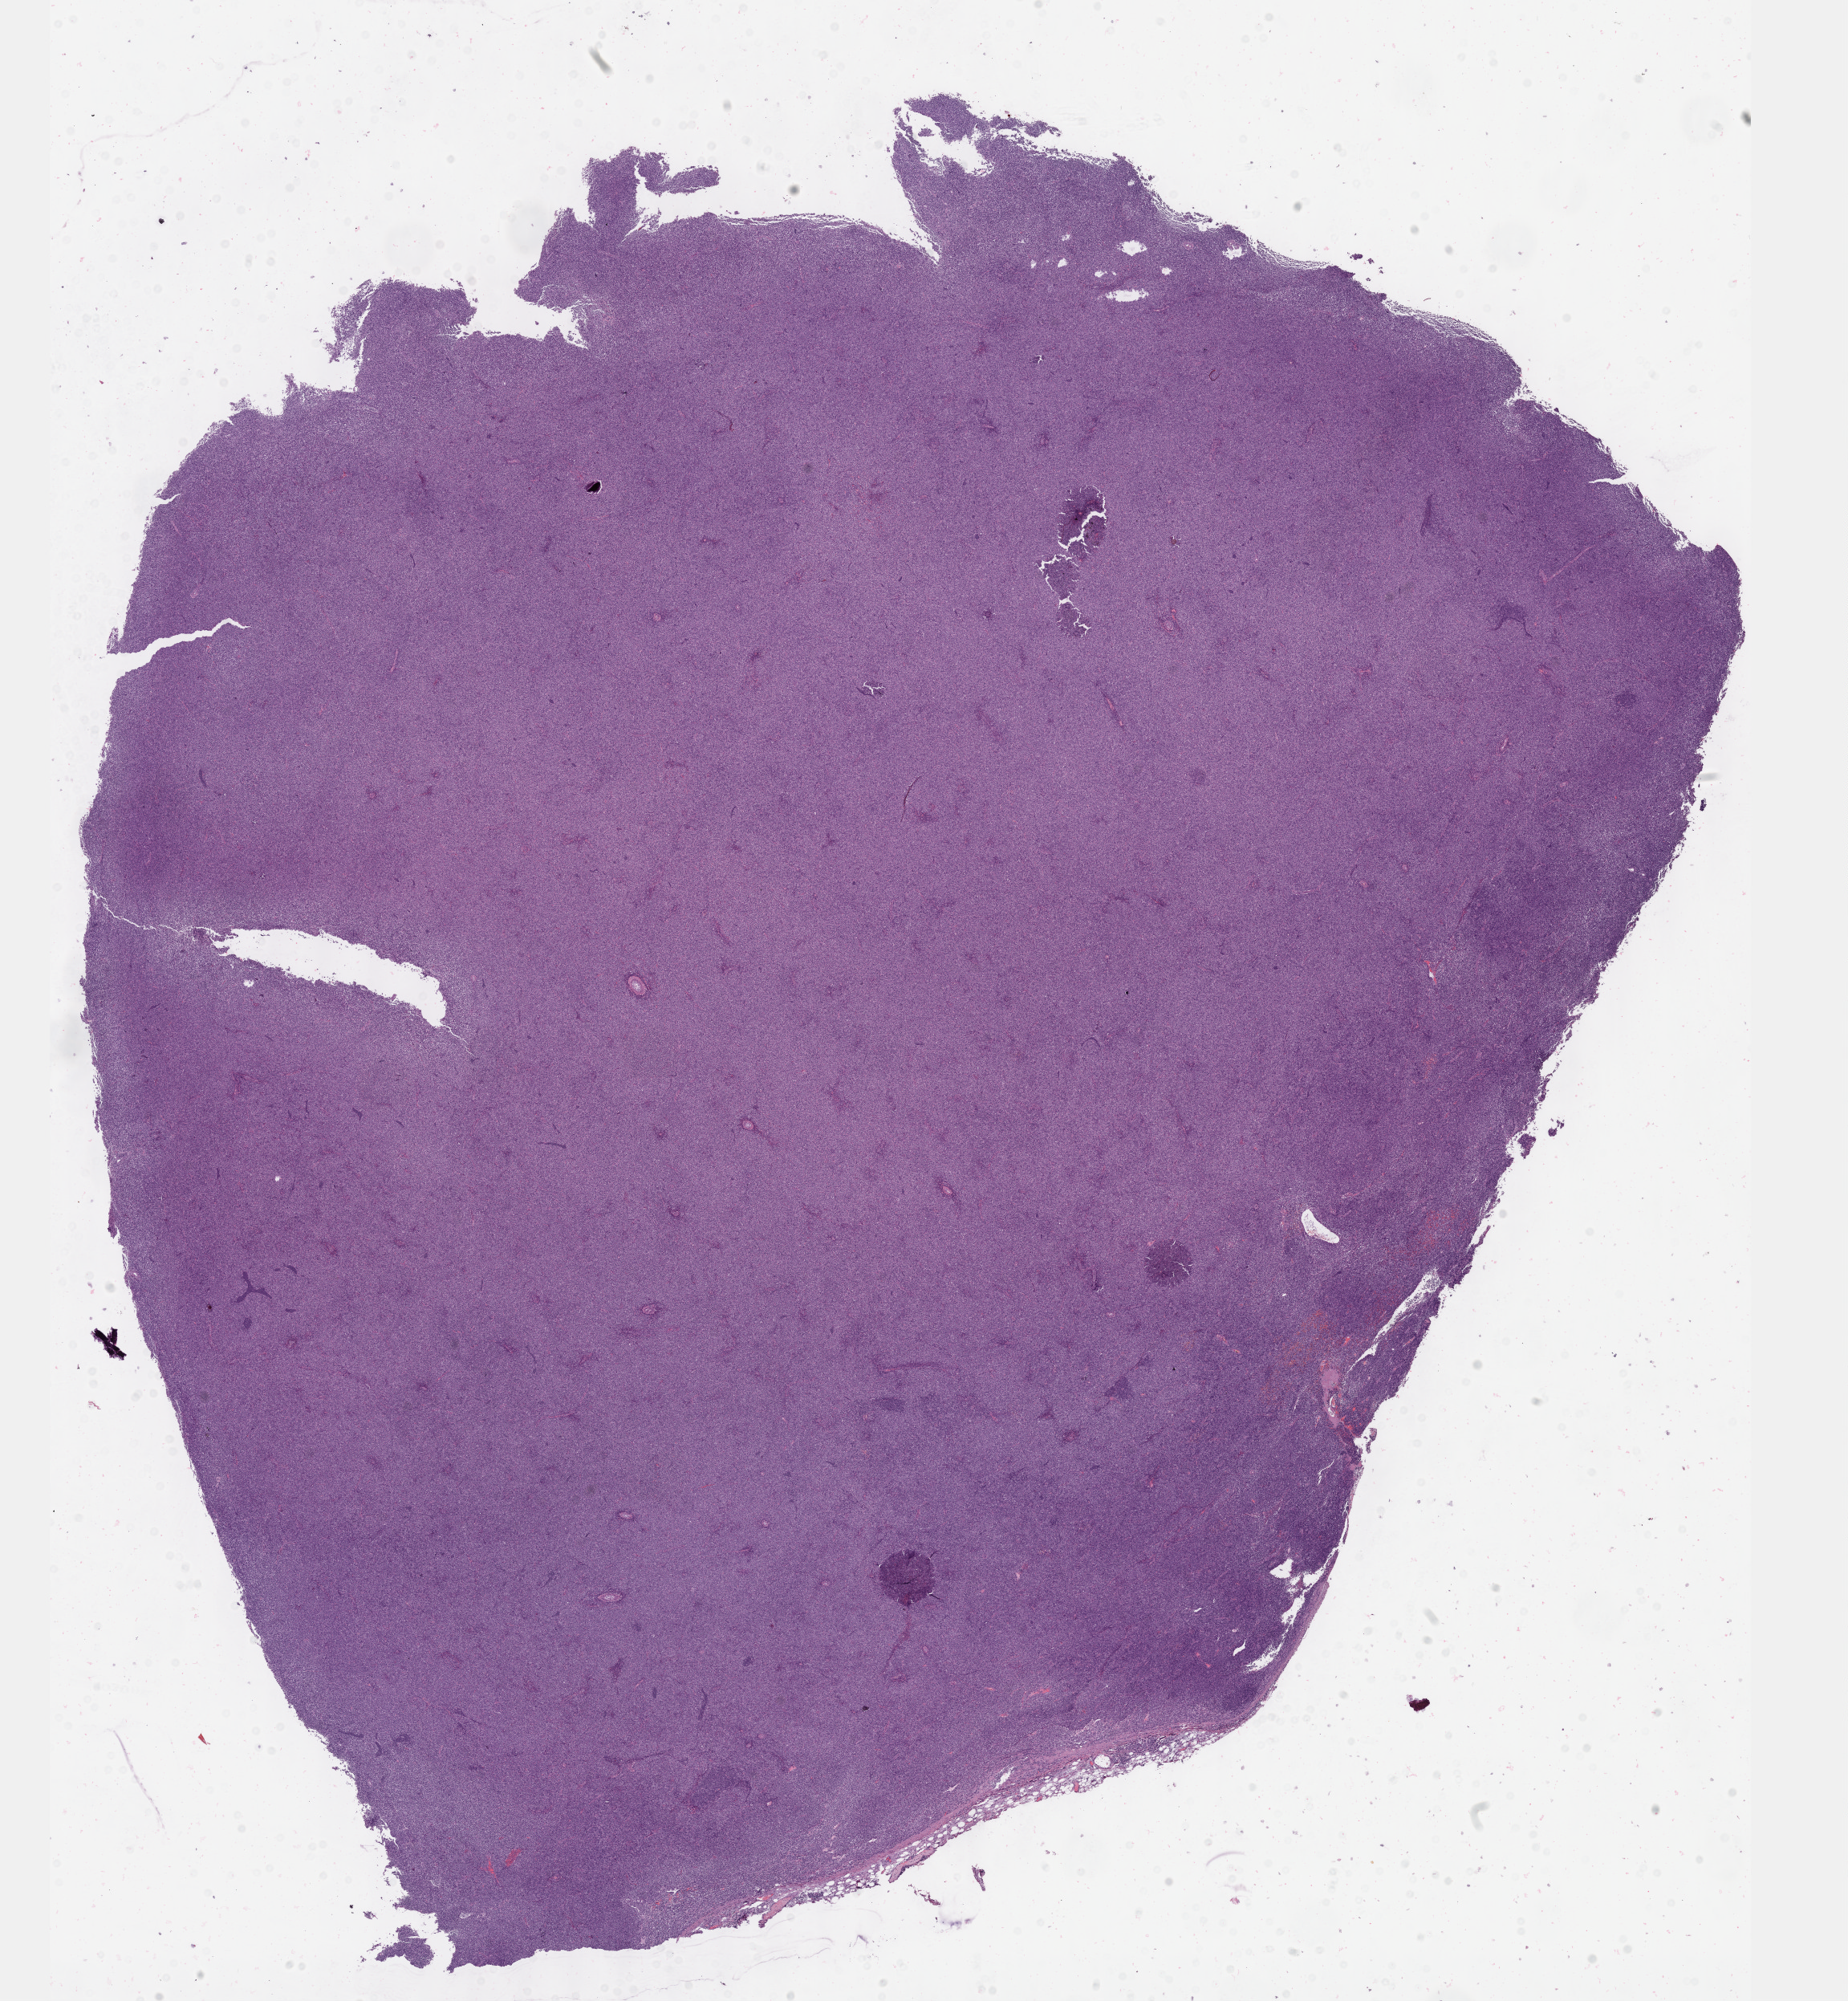
Digitized H&E tissue section (whole slide) — a low-resolution overview of the entire scanned area, about 18.6 x 20.1 mm (from a 40x scan); formalin-fixed paraffin-embedded (FFPE) diagnostic section; primary tumour sample from the lymphoid tissue. Patient: male, age at initial diagnosis 37 years.
Histologic diagnosis: Diffuse large B-cell lymphoma, NOS (lymph nodes of inguinal region or leg).